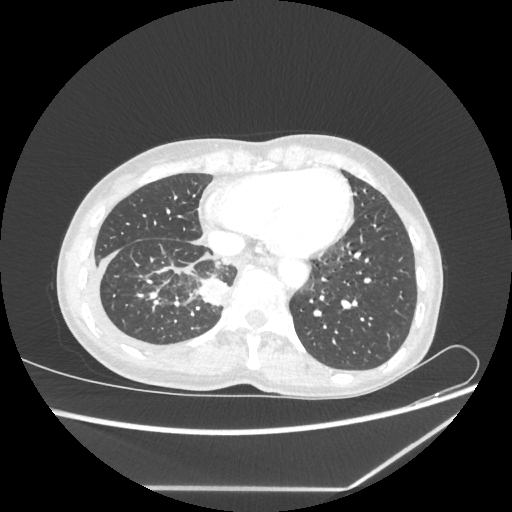
Chest CT, one axial slice. Position 66 of 237 along the scan axis. Lung window (W 1500 / L -600 HU). 1.25 mm slice thickness. 512 × 512 image matrix, field of view 364 × 364 mm. Female patient, age 59 years. Case-level facts recorded for this patient, not image findings: clinical TNM (as recorded): T1c N1 M1.
Outlined on this slice (rectangle marked by the reading radiologist):
- lung tumour (recorded histology: adenocarcinoma): bounding box <198,276,228,309> (left, top, right, bottom; pixels)